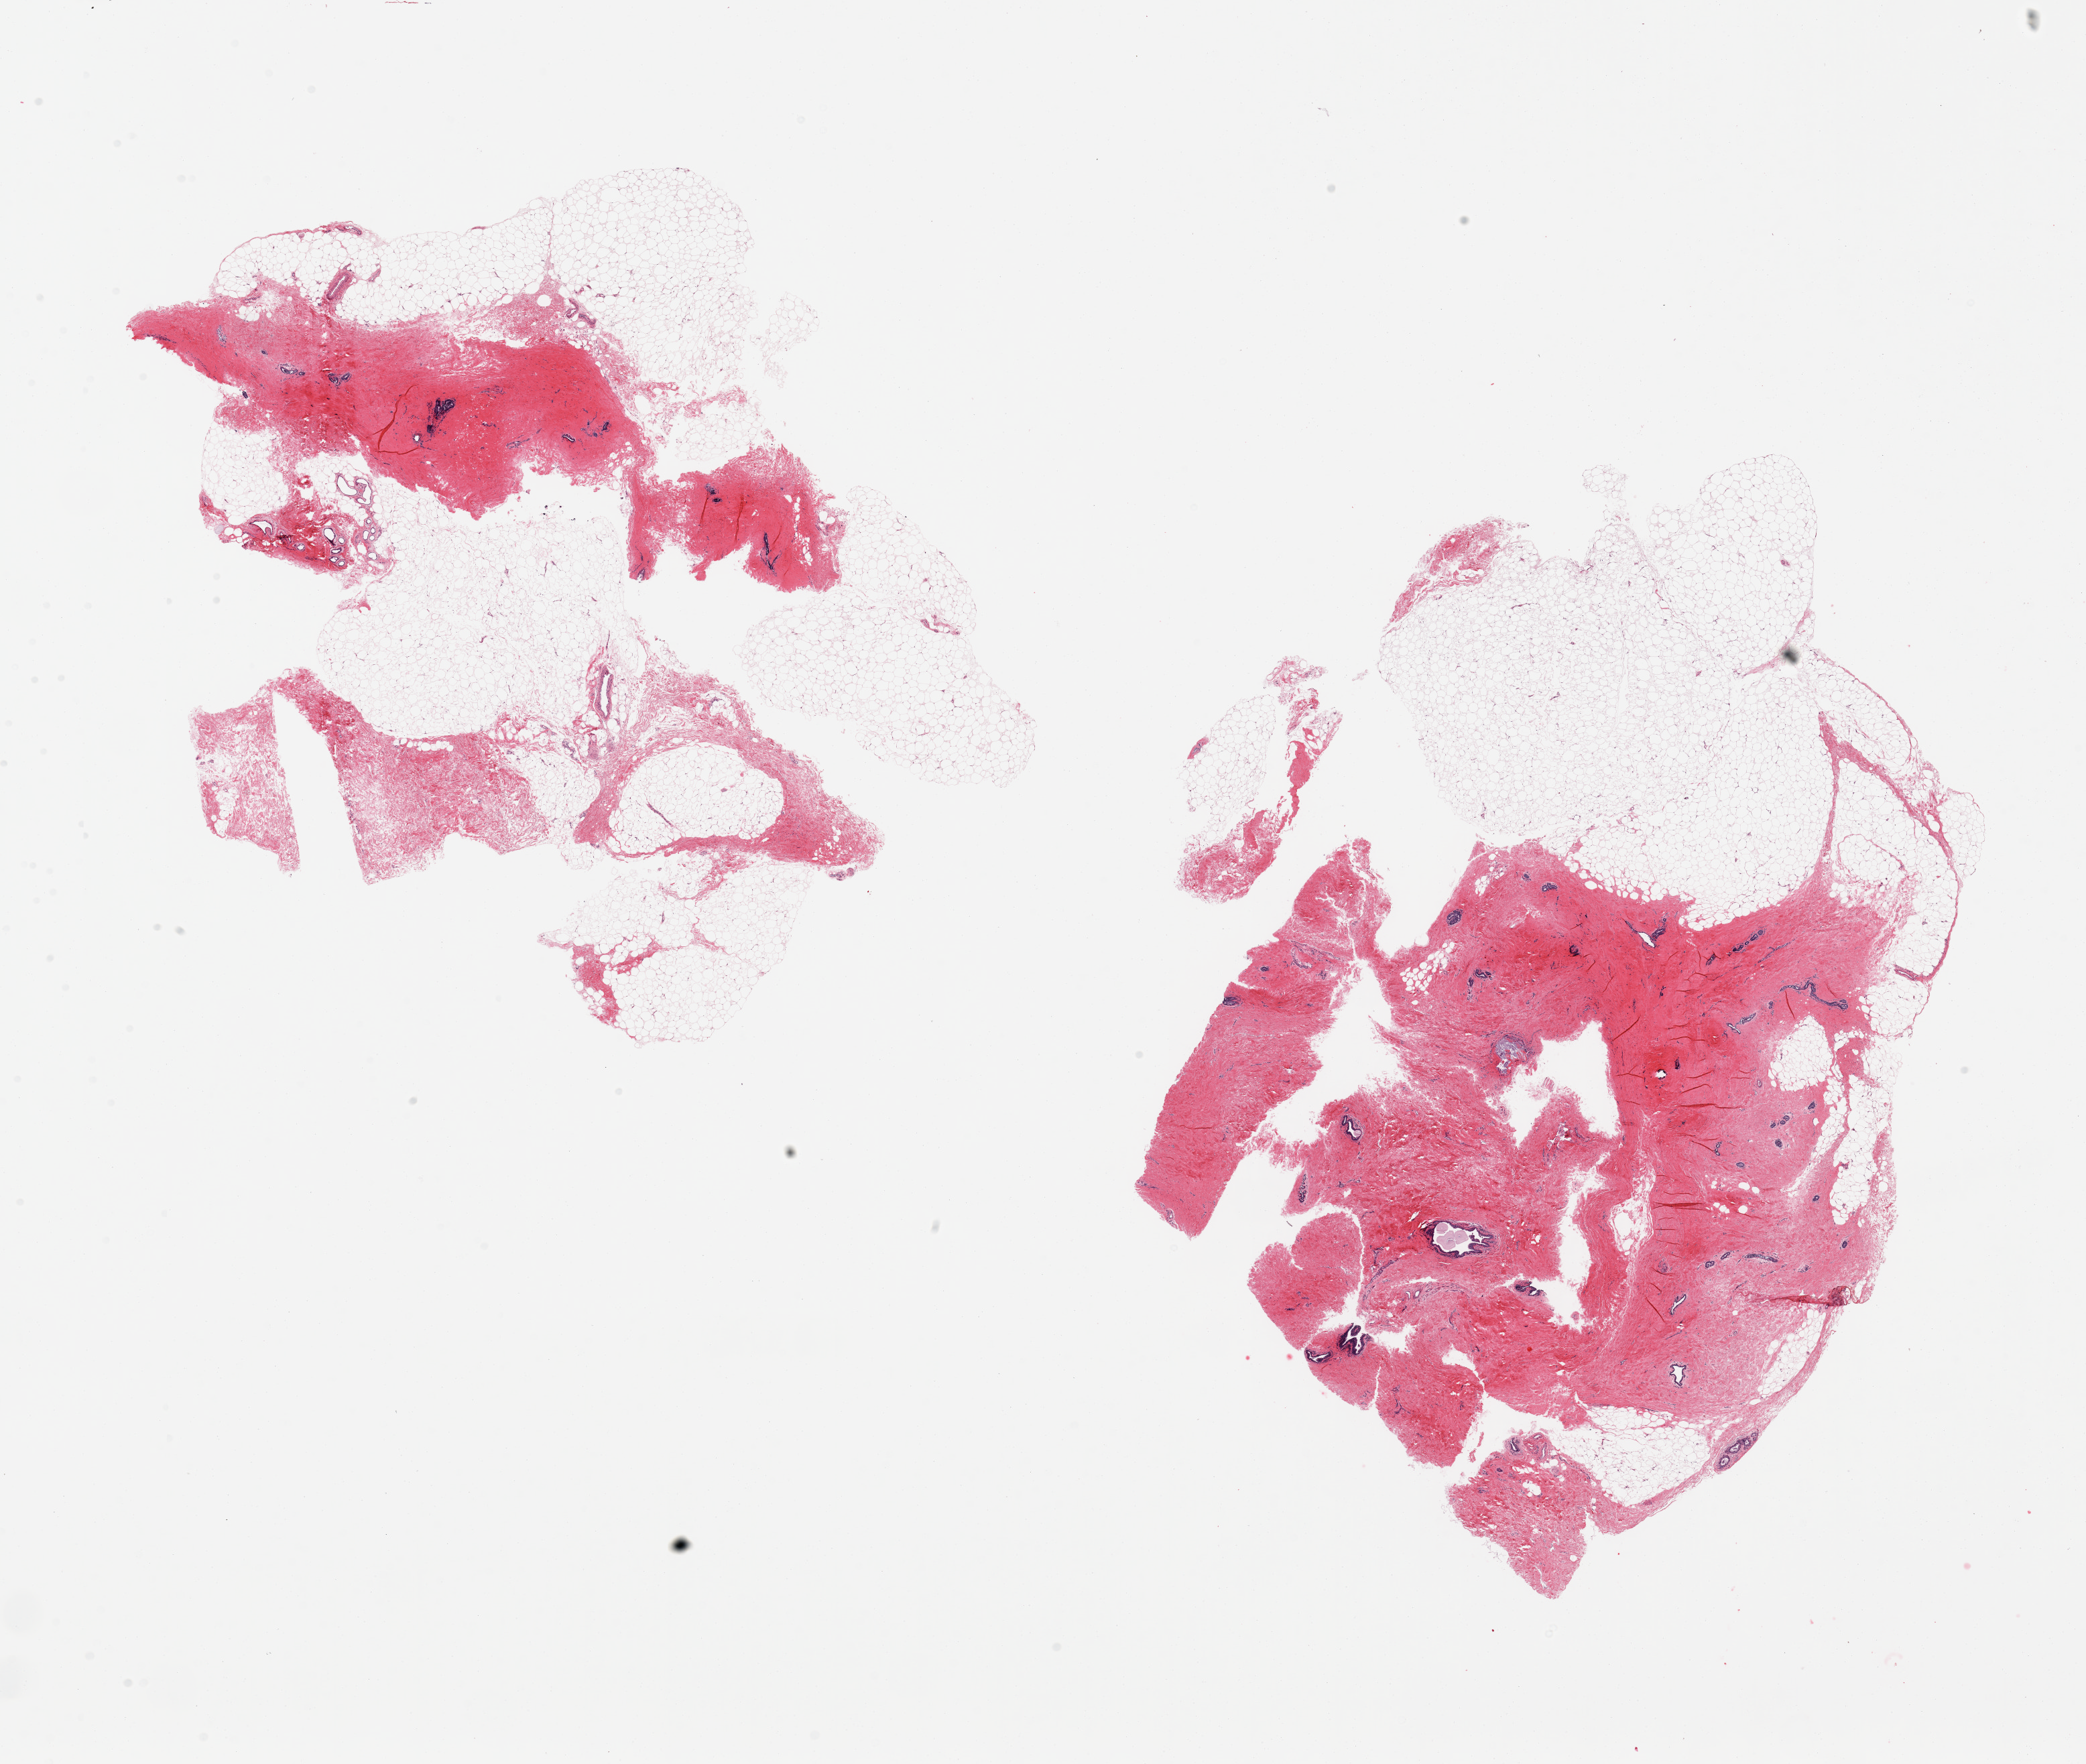
Whole-slide image, H&E stain, brightfield — a low-resolution overview of the entire scanned area, about 24.6 x 20.8 mm, PAXgene-fixed, paraffin-embedded tissue, section of breast (target tissue), donor tissue sample. Male donor.
• pathologist's review note for this sample: 2 pieces, gynecomastoid stromal hyperplasia; ductal elements